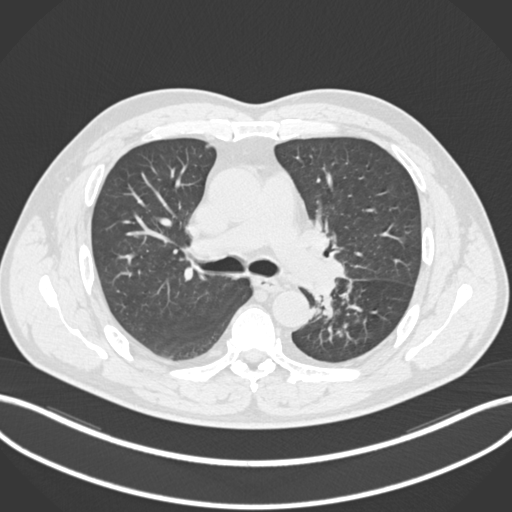
Chest CT, one axial slice; reconstruction kernel B30f; 120 kVp; lung window (W 1500 / L -600 HU); 1 mm slice thickness; 512 × 512 image matrix, field of view 400 × 400 mm. Patient: male, 50 years. Case-level facts recorded for this patient, not image findings: clinical TNM (as recorded): T2a N3 M0.
Outlined on this slice (rectangle marked by the reading radiologist):
- lung tumour (recorded histology: squamous cell carcinoma): bounding box (x1, y1, x2, y2) in pixels: (305, 278, 339, 303)